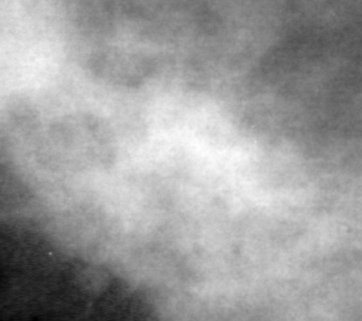
Crop from a digitized film mammogram around one marked abnormality; left breast; MLO view; BI-RADS breast density category 4 (scale 1–4).
- Finding: mass, shape irregular, margins spiculated; BI-RADS assessment category 5; subtlety rating 2 on a 1 (subtle) to 5 (obvious) scale; pathology result (as recorded, not read from the image): benign.